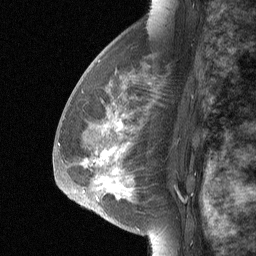
Breast MRI (dynamic contrast-enhanced), one sagittal slice; slice 40 of 64 in the series (ordered by position); dynamic contrast-enhanced study with each time point stored as its own series, time point 2 of 3 at this slice position (early post-contrast, ordered by acquisition time); 1.5 T; TE 4.8 ms, TR 27 ms; 2 mm slice thickness; 256 × 256 image matrix. Female patient, age 56 years. From the clinical record (not read from this slice): setting: breast cancer imaged before/during neoadjuvant chemotherapy; receptor status: HER2-positive.
Structures marked on this image (semi-automatic segmentation, software-assisted and operator-edited):
- analysis volume of interest (the breast-tissue region the enhancement analysis was run in; not a lesion): bounding box [x1, y1, x2, y2] px = [68, 83, 168, 214]
- tumour enhancement mask (voxels above the 90 % enhancement threshold inside the analysis volume of interest): [102, 126, 120, 190]